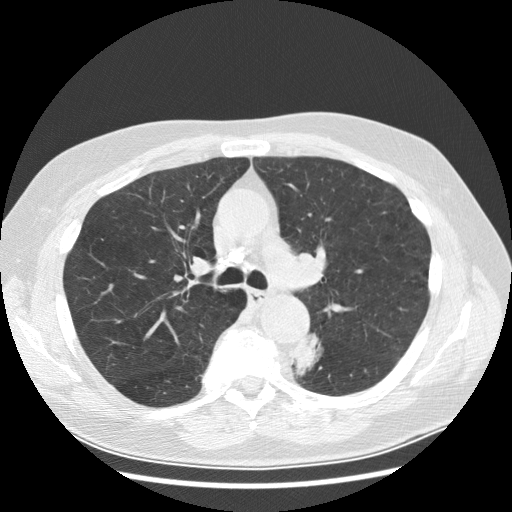
Axial slice from a low-dose chest CT screening exam. First (baseline) screen. Lung window (W 1500 / L -600 HU). 2.5 mm slice thickness. Slice 96 of 282 in the series. 512 × 512 image matrix. Male participant, aged 70 years at enrolment. Current smoker at enrolment.
• Expert-annotated lung lesion, box from (x=277, y=336) to (x=326, y=380) px.
• Screening reader's record for this exam (one nodule recorded; not confirmed to be the boxed lesion): non-calcified nodule or mass ≥4 mm, left lower lobe, 27 × 16 mm, spiculated (stellate) margins, soft tissue attenuation, pre-existing on the prior screen: yes; interval growth: yes.
• Official screen result: positive, change unspecified: nodule(s) >= 4 mm or enlarging nodule(s), mass(es), or other non-specific abnormalities suspicious for lung cancer.
• Later outcome: lung cancer diagnosed 97 days after this screen — papillary adenocarcinoma, NOS, left lower lobe, moderately differentiated (G2), stage IB (AJCC 6th edition), 35 mm at pathology.